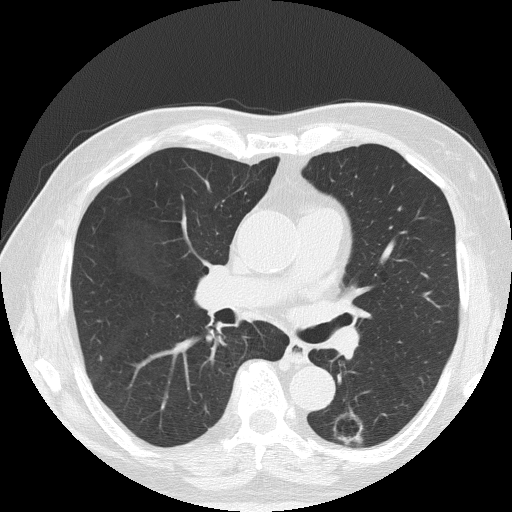
Axial slice from a low-dose chest CT screening exam. Baseline screening round. Lung window (W 1500 / L -600 HU). 2 mm slice thickness. Slice 73 of 145 in the series. Male participant, aged 71 years at enrolment.
• Lesion marked by an expert reader, bounding box (x1, y1, x2, y2) in pixels: (321, 408, 375, 452).
• Screening reader's record for this exam: no non-calcified nodule ≥4 mm recorded.
• Lung cancer was diagnosed 340 days after this screen: adenocarcinoma, NOS, left lower lobe, poorly differentiated (G3), stage IA (AJCC 6th edition), 28 mm at pathology.